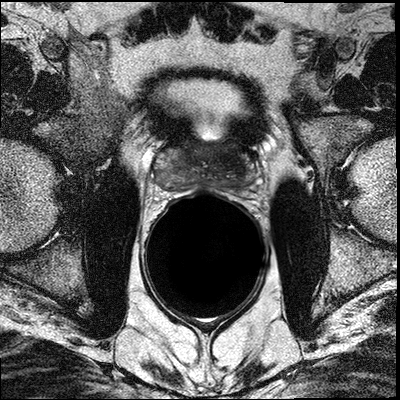
MRI of the prostate; 3 images, each a single mid-volume slice chosen by position (not for content).
Image 1: axial T2-weighted image, series "T2W_TSE_AX", slice 21 of 40.
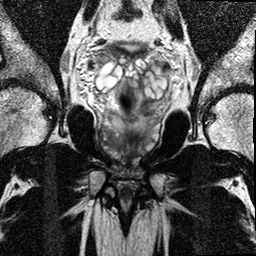
Image 2: coronal T2-weighted image, series "T2W_TSE_COR", slice 13 of 24.
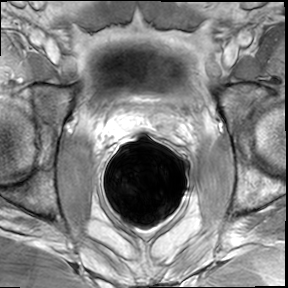
Image 3: axial dynamic contrast-enhanced (DCE) T1-weighted image, series "AX BLISS_GAD_8", slice 19 of 36, dynamic phase 5 of 8, 6 mm slice thickness.
MRI report (verbatim):
prostate has a maximal lateral diameter of 4.5 cm, a maximal craniocaudal diameter of 4.2 cm and a maximal AP diameter of 2.8 cm resulting in an estimated gland volume of 28 cc. The zonal anatomy is preserved. In the mid third of the prostate, in the right posterior lateral peripheral zone between 6:00 and 10:00 there is a geographic 2.0 x 1.8 cm hypointense mass seen which shows rapid wash-in and washout on the dynamic series.(slice location 39; series 501; 401 and 701-709). There is bulging of the tumor at 8-10 o'clock towards the pubo-rectal sling, which seems not to be involved since there is a thin fatty line preserved between tumor and muscle. No manifest extraprostatic tumor mass seen. ("capsular infiltration" is likely). The right neuro vascular bundle seems not to be involved. The tumor extends to the apical and upper third of the prostate. No evidence for involvement of the neurovascular bundle on either side. No evidence for seminal vesicles infiltration. No evidence of involvement of bladder neck and rectal wall. No suspiciously enlarged obturator and iliac lymph nodes. Multiplanar reconstructions, subtraction images, and CAD analysis of the dynamic series for assessment of the kinetic information facilitated the interpretation of the exam;performed by radiologist. IMPRESSION: 2 cm bulging mass in the right posterior and lateral peripheral zone of the midthird of the prostate, with extension into the upper third and lower (apical third); with likely "capsular infiltration" in proximity to the right pubo-rectal sling (at level of mid third) , without manifest extracapsular extension. No evidence of neurovascular bundles involvement. No seminal vesicles infiltration.

Biopsy pathology report for this patient (as recorded):
The specimen consists of multiple core fragments of tan soft tissue measuring 0.8cm to 1.5cm in length and 0.1cm in diameter. The specimen is submitted entirely in six cassettes. 1-right pz, 2-right pz/tz, 3-right apex, 4-left pz, 5-left pz/tz, 6-left apex. PROSTATE: 1-RIGHT PZ: PROSTATIC ADENOCARCINOMA, GLEASON SCORE 4+4=8/10, INVOLVING 50% OF THE TISSUE REPRESENTED. 2-RIGHT PZ/TZ: PROSTATIC ADENOCARCINOMA, GLEASON SCORE 4+3=7/10, INVOLVING 80% OF THE TISSUE REPRESENTED. 3-RIGHT APEX: PROSTATIC ADENOCARCINOMA, GLEASON SCORE 4+3=7/10, INVOLVING 50% OF THE TISSUE REPRESENTED. 4-LEFT PZ: PROSTATIC TISSUE. NO TUMOR IDENTIFIED. 5-LEFT PZ/TZ: PROSTATIC TISSUE. NO TUMOR IDENTIFIED. 6-LEFT APEX: PROSTATIC TISSUE. NO TUMOR IDENTIFIED.